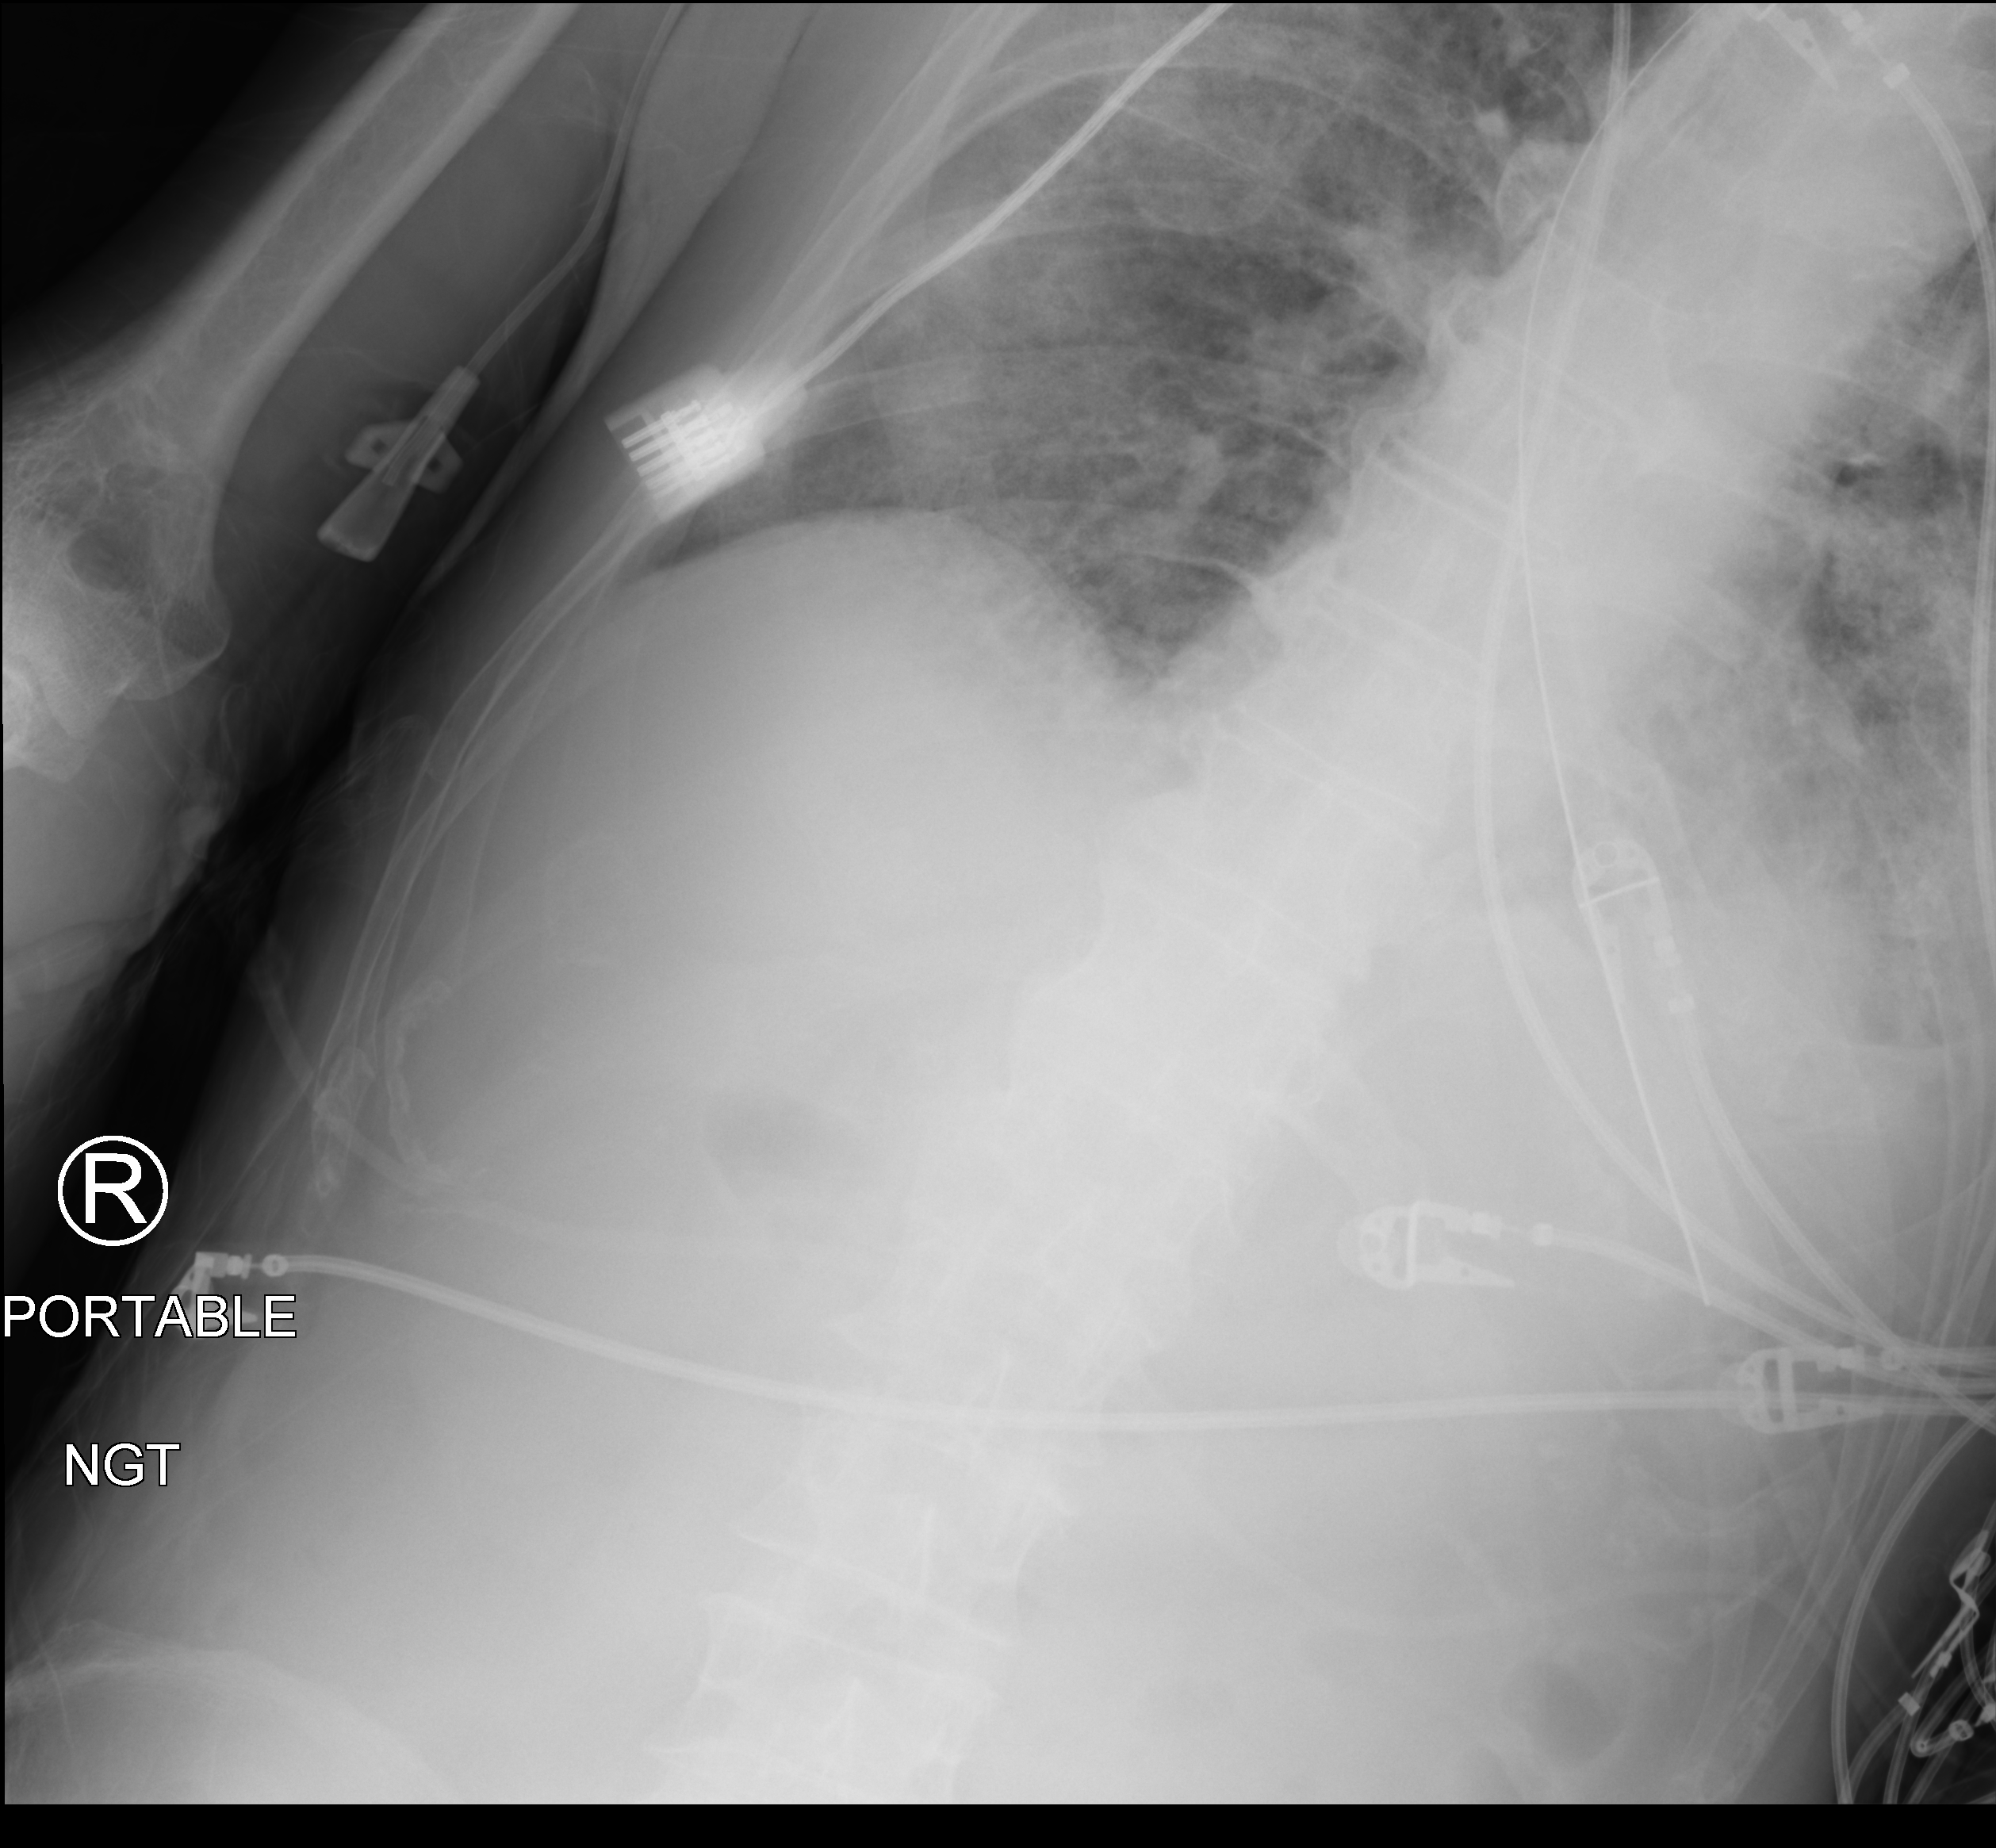
Bedside chest radiograph (computed radiography), anteroposterior (AP) projection. Male patient hospitalised with COVID-19, age 60–74 years.
Hospital-stay facts (about this admission, not read from this image; timing relative to this image not recorded): mechanically ventilated during this hospital stay: yes; admitted to intensive care during this hospital stay: yes; diabetes (admission record): yes.